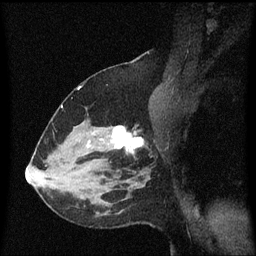
Breast MRI (dynamic contrast-enhanced), one sagittal slice. Slice 38 of 60 in the series (ordered by position). Dynamic contrast-enhanced series, image 2 of 3 at this slice position (ordered by acquisition). 1.5 T. TE 4.2 ms, TR 8.4 ms. 2 mm slice thickness. 256 × 256 image matrix, field of view 200 × 200 mm. Patient: female, 37 years. From the clinical record (not read from this slice): setting: breast cancer imaged before/during neoadjuvant chemotherapy; receptor status: HR-positive, HER2-negative.
Outlined on this slice (semi-automatically segmented with operator editing):
- analysis volume of interest (the breast-tissue region the enhancement analysis was run in; not a lesion): bounding box (x1, y1, x2, y2) in pixels: (95, 126, 151, 171)
- tumour enhancement mask (voxels above the 70 % enhancement threshold inside the analysis volume of interest): (102, 126, 144, 153)